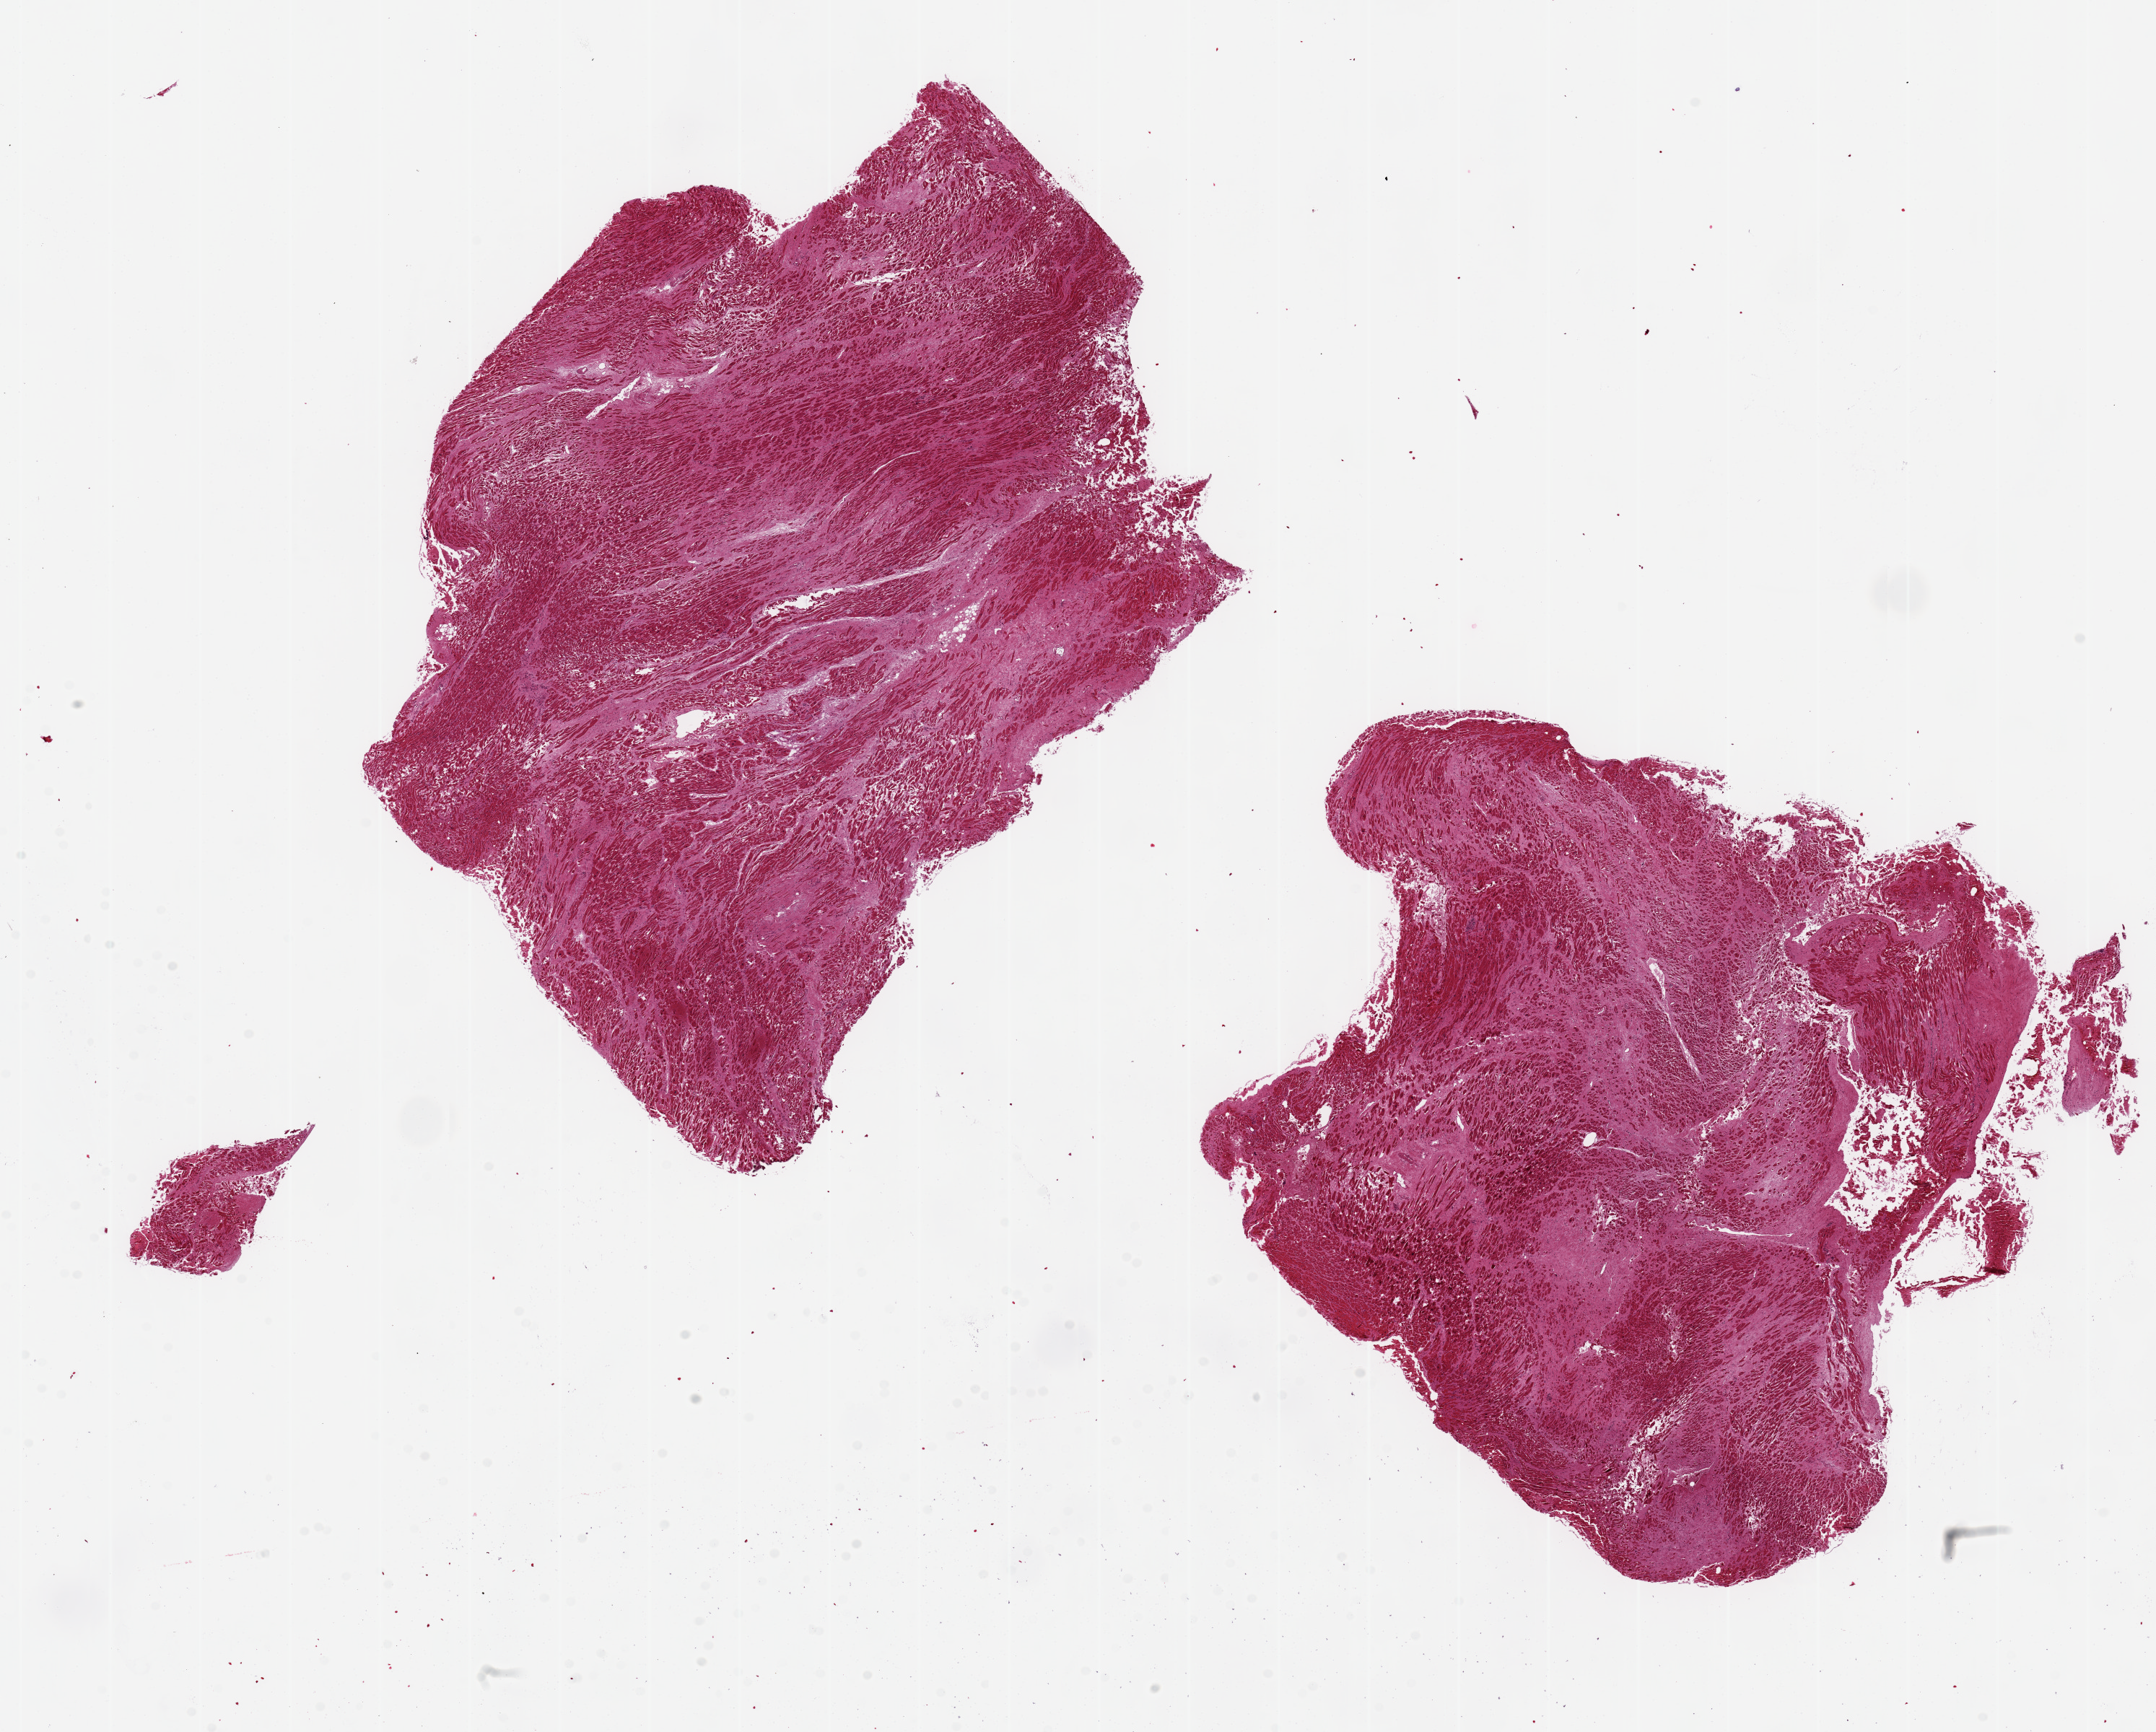
Haematoxylin and eosin whole-slide image, a low-resolution overview of the entire scanned area, about 23.6 x 19.0 mm; PAXgene-fixed, paraffin-embedded tissue; sampled site (target tissue): heart; donor tissue sample. Donor: female.
* reviewer comment on this tissue sample: 2 ~9x7mm aliquots. Extensive interstititial fibrosis/infarcts